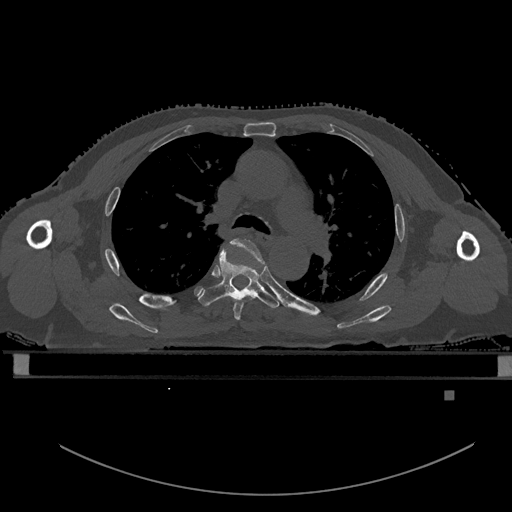
CT including the spine, one axial slice. Slice 374 of 969 in the series (ordered by position). Bone window (W 1800 / L 400 HU). 0.5 mm slice thickness. 512 × 512 image matrix. Male patient, age 82 years. Case-level facts recorded for this patient, not image findings: primary cancer: prostate; vertebrae with lytic lesions (as recorded): T11, T9, T8, T2.
Structures marked on this image (semi-automatic segmentation, software-assisted and operator-edited):
- T4 vertebra: box from (x=231, y=238) to (x=265, y=320) px
- T5 vertebra: (x=199, y=249)–(x=281, y=308)